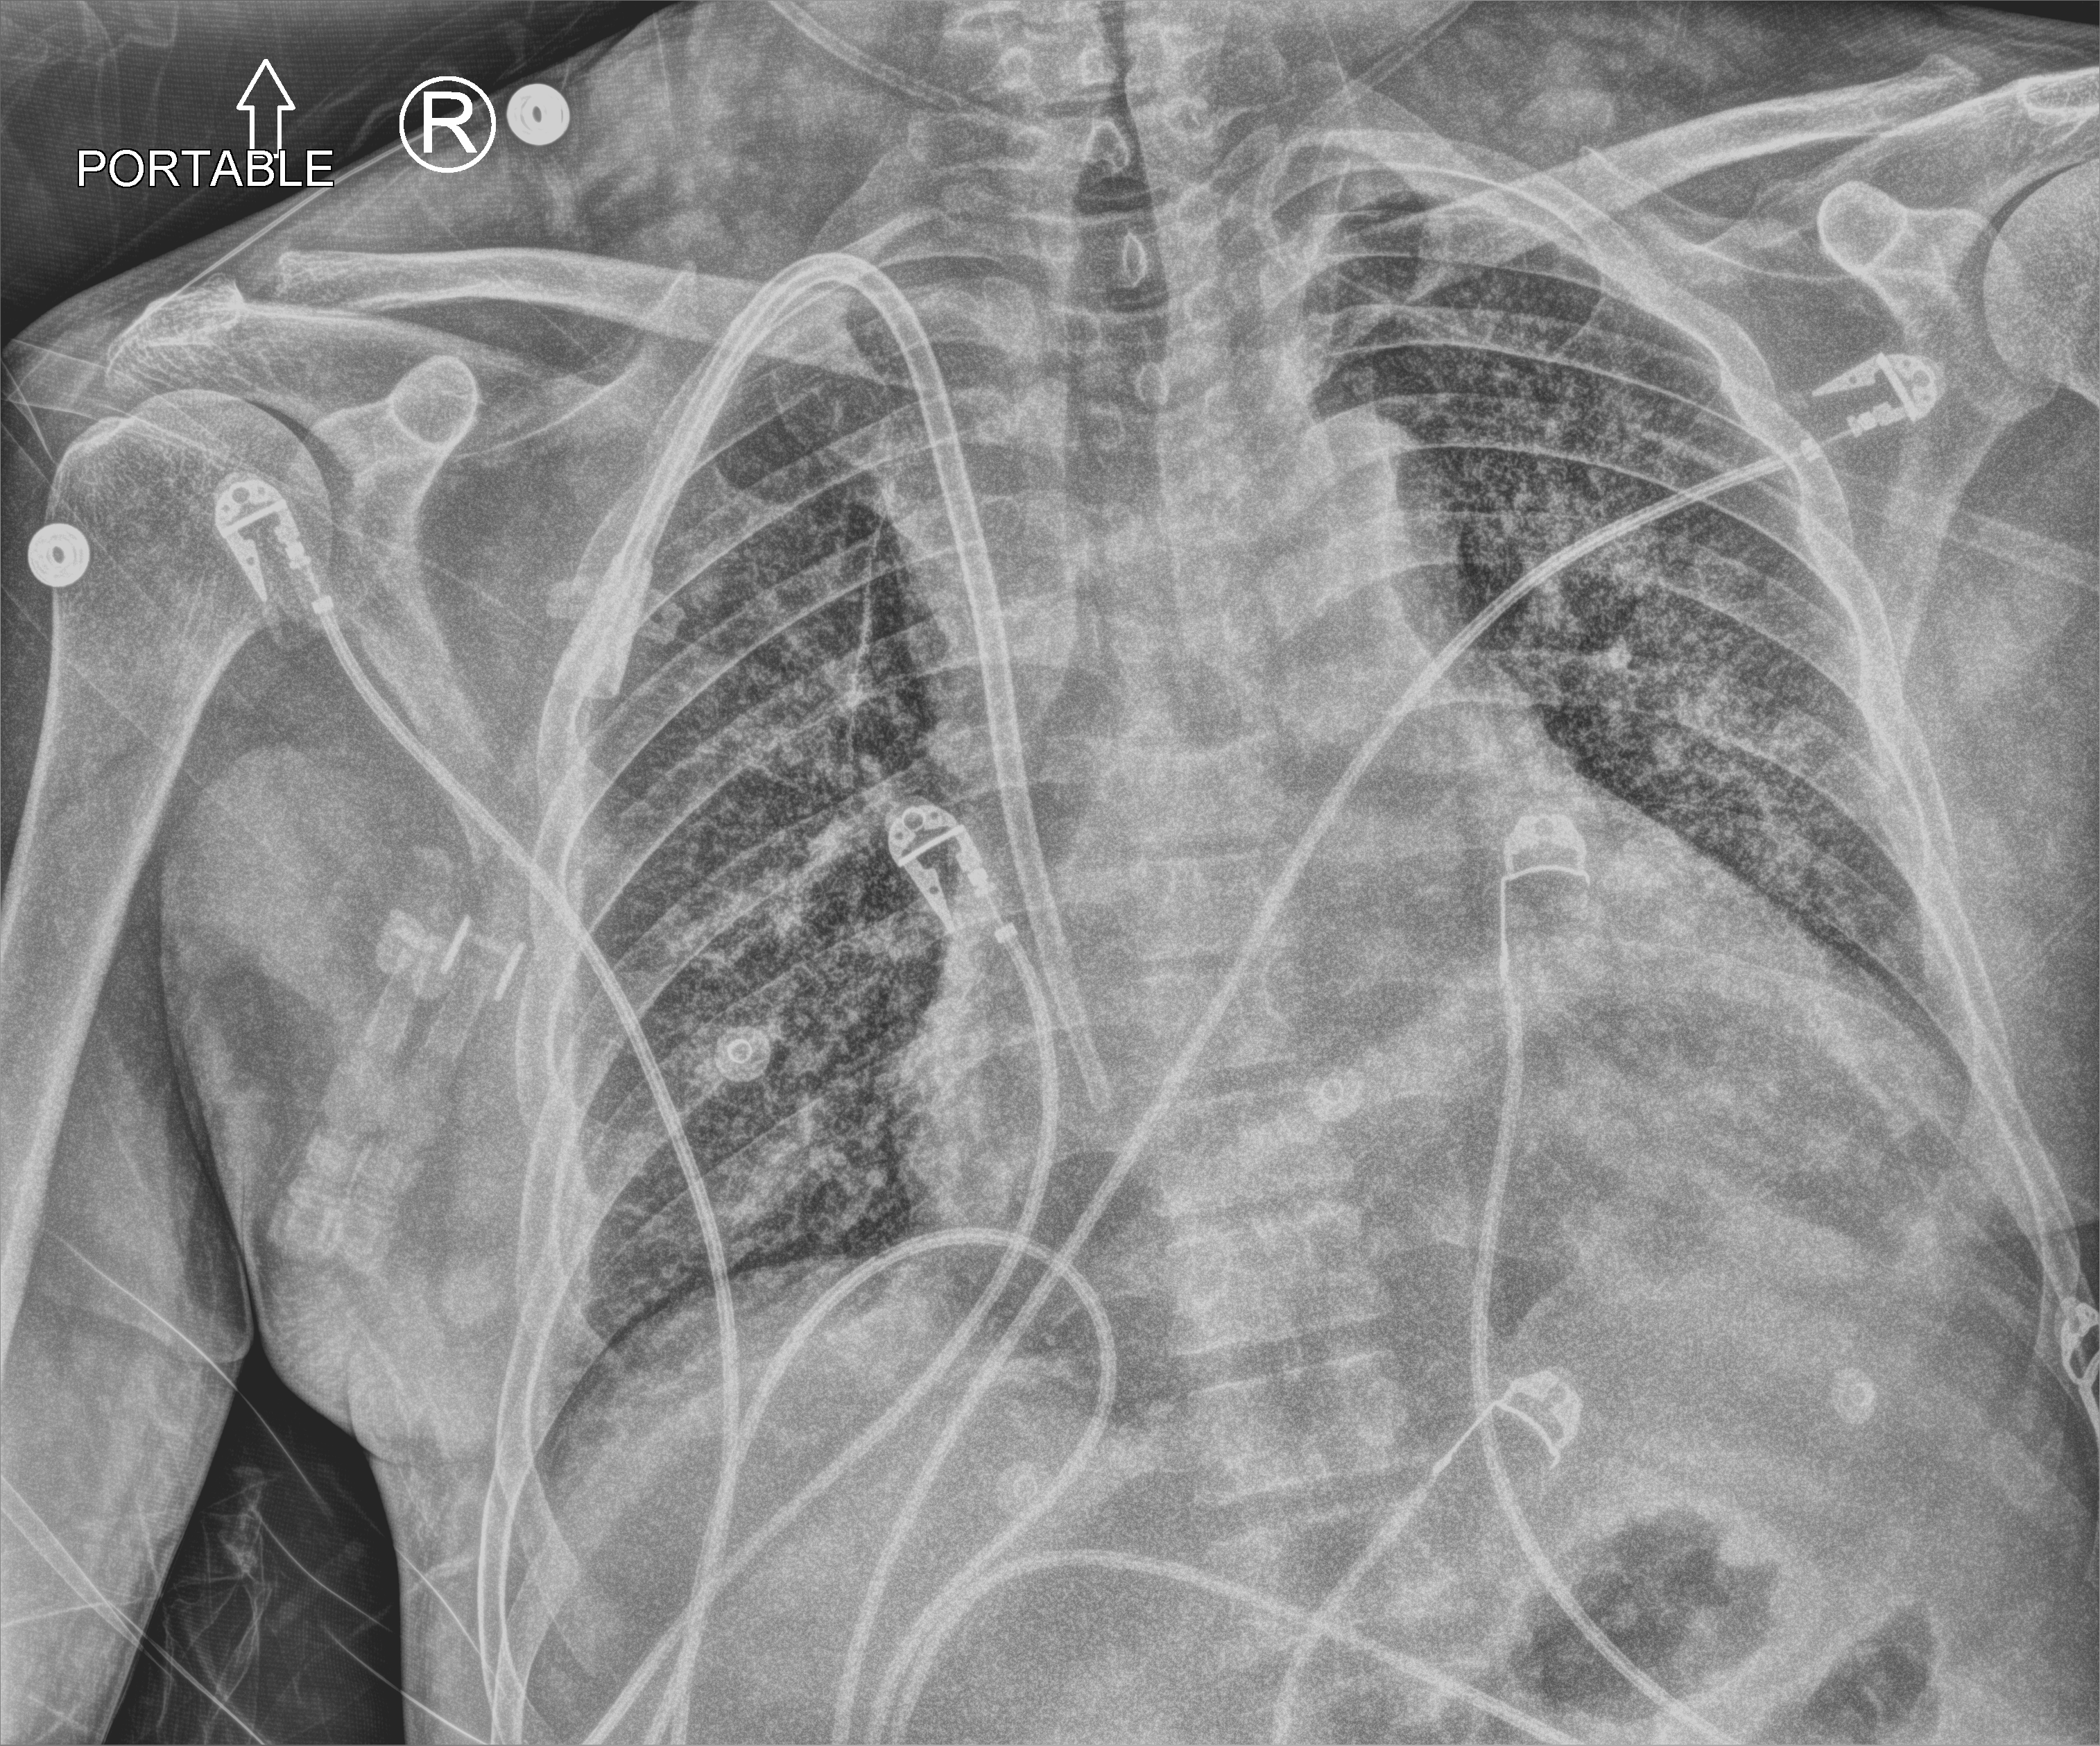
Bedside chest radiograph (computed radiography), anteroposterior (AP) projection. Male patient hospitalised with COVID-19, age 18–59 years.
Admission-level facts for this patient (not findings on this image; timing relative to this image not recorded):
- admitted to intensive care during this hospital stay: no